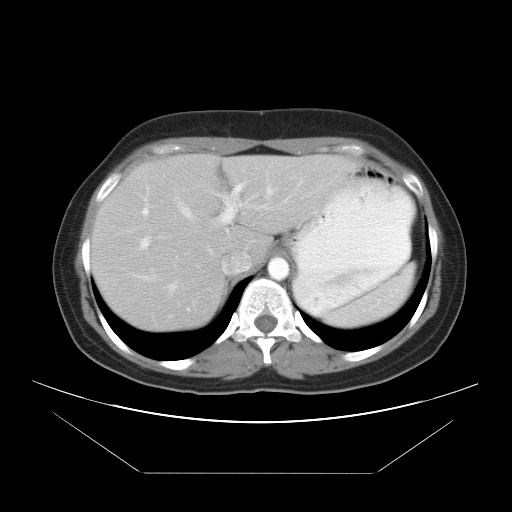
Contrast-enhanced abdominal CT, one axial slice. Slice 28 of 34 in the series (ordered by position). Reconstruction kernel STANDARD. 120 kVp. Intravenous contrast given. Soft-tissue window (W 400 / L 40 HU). 7.5 mm slice thickness. 512 × 512 image matrix. Female patient, age 38 years. From the clinical record (not read from this slice): diagnosis: colorectal cancer liver metastases, imaged before liver resection; multiple liver metastases: yes; largest metastasis: 3.1 cm.
Structures marked on this image (expert manual segmentation):
- hepatic veins: bounding box [x1, y1, x2, y2] px = [141, 189, 272, 295]
- liver: [91, 154, 357, 333]
- planned liver remnant (the part of the liver to remain after resection): [198, 155, 358, 262]
- portal vein (with intrahepatic branches): [141, 185, 340, 248]